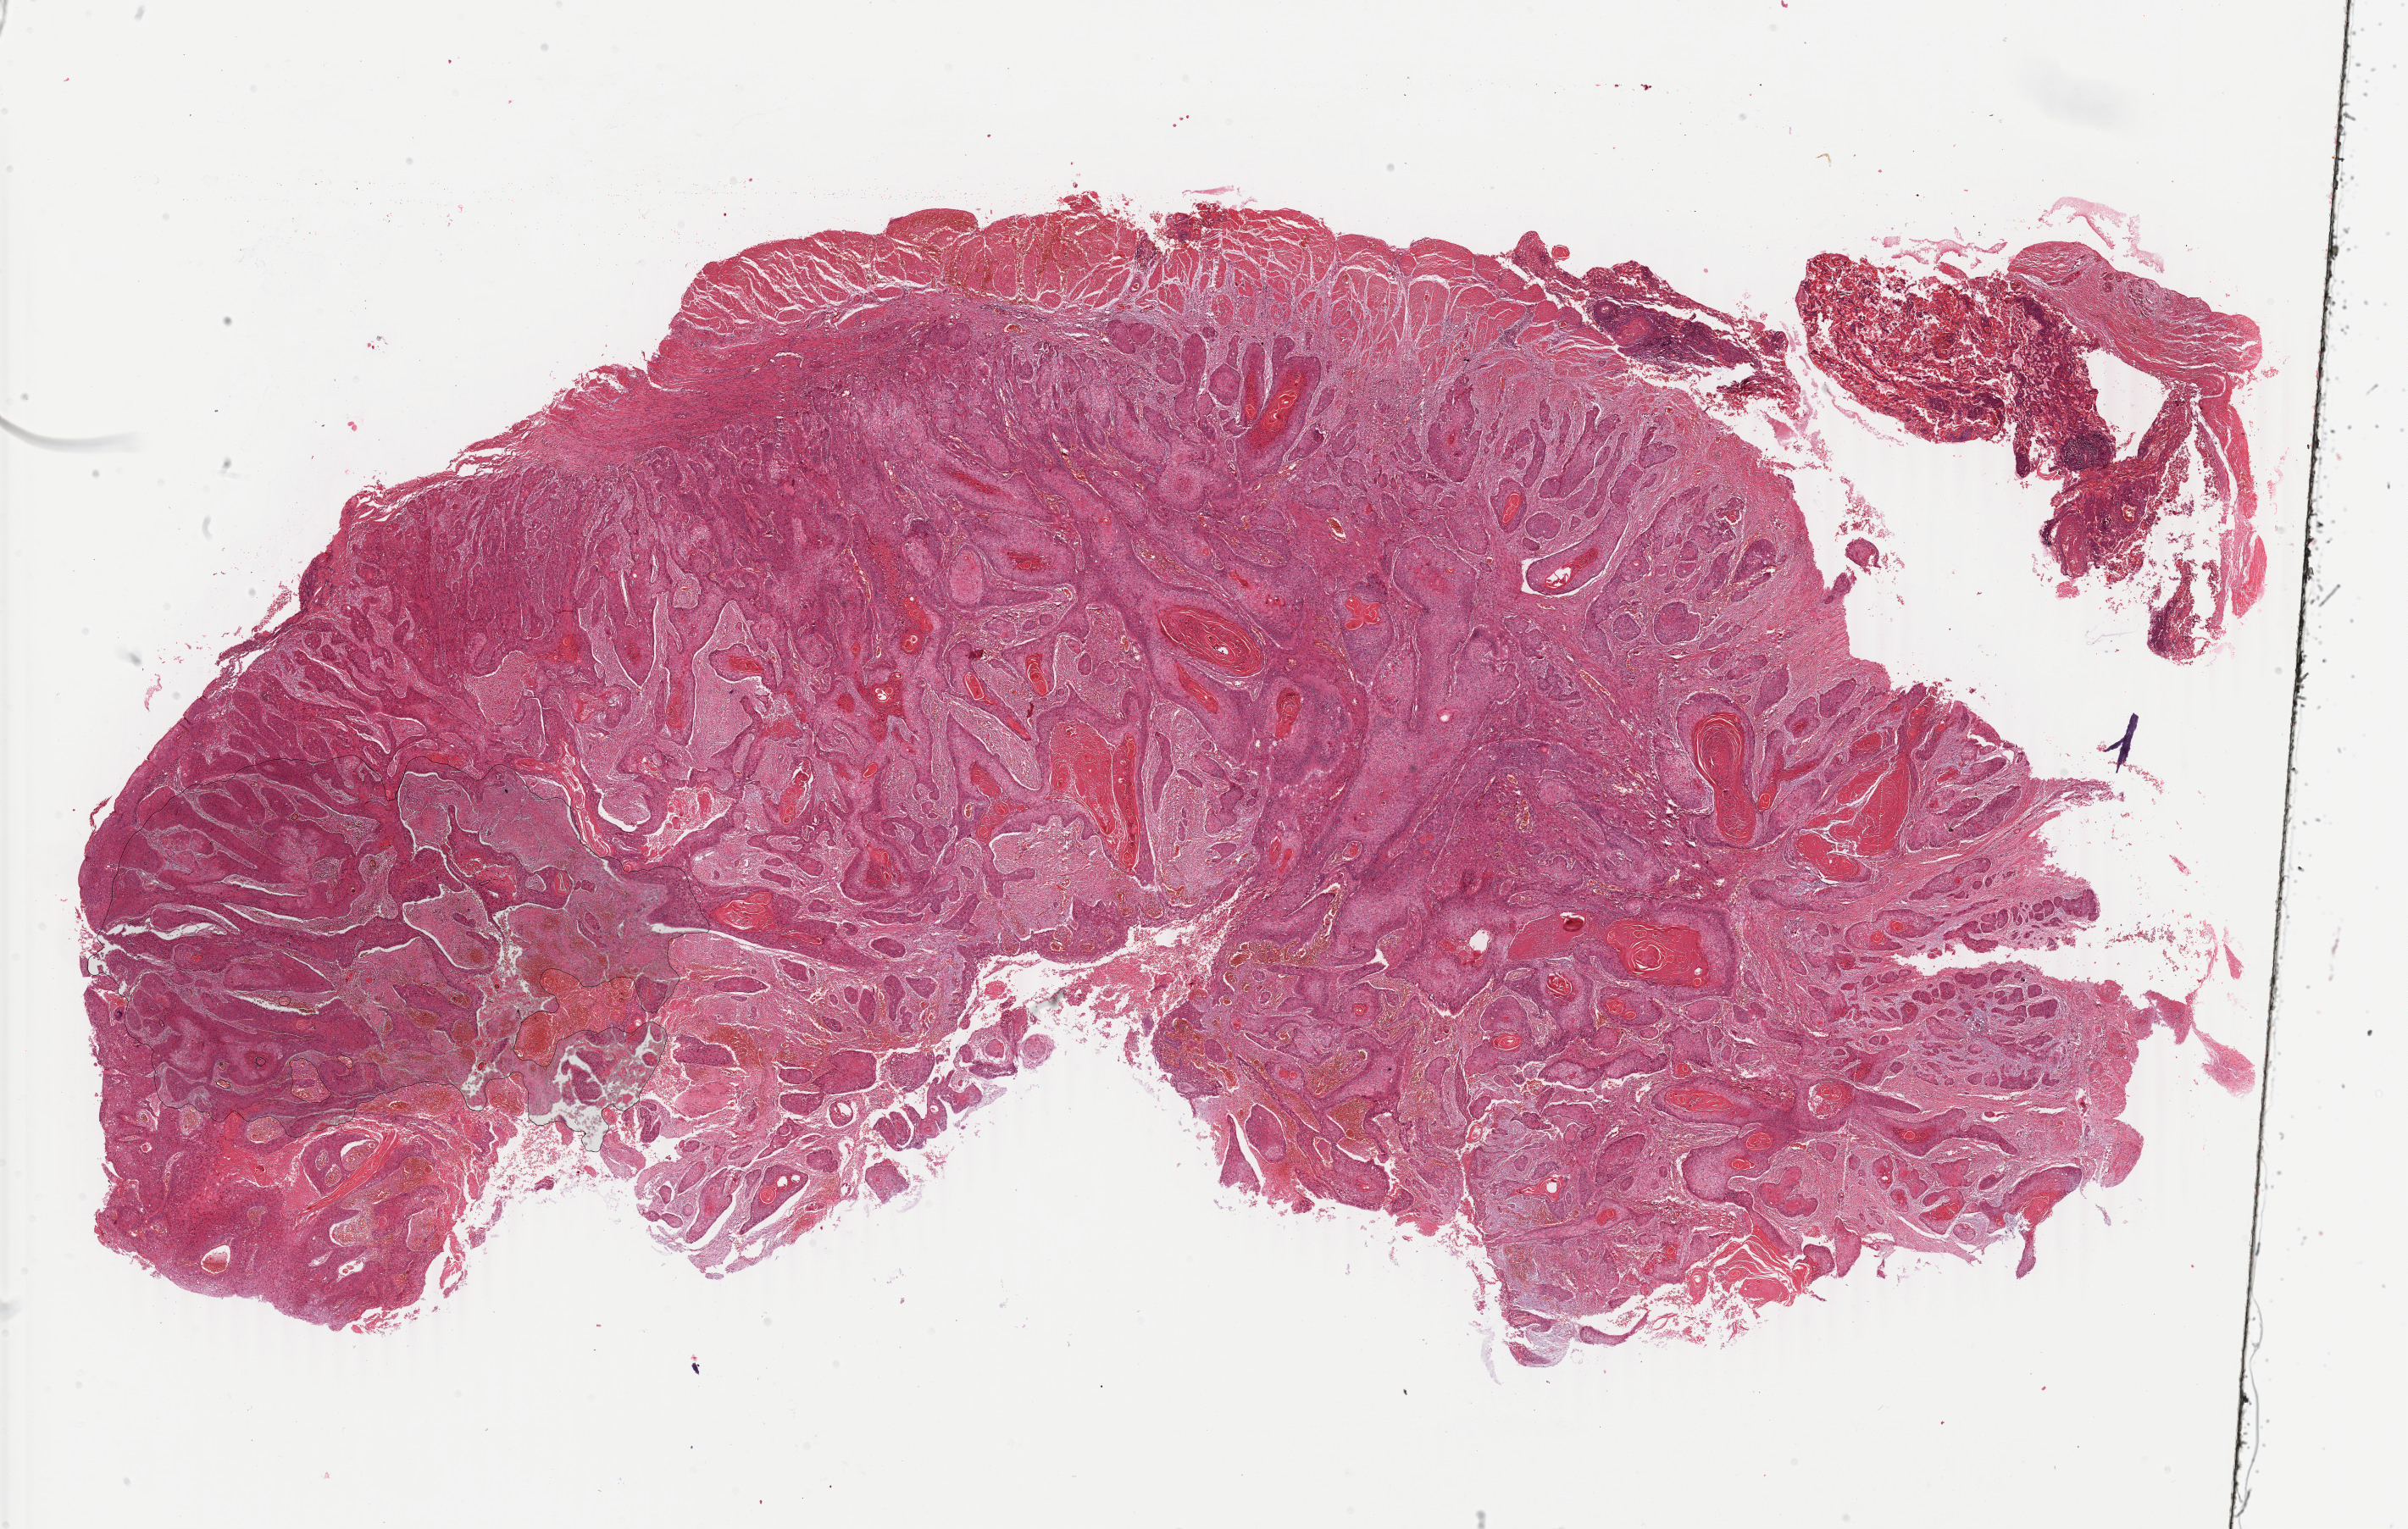
Hematoxylin and eosin (H&E) stained whole-slide image, a low-resolution overview of the entire scanned area, about 22.6 x 14.4 mm (from a 40x scan). Formalin-fixed paraffin-embedded (FFPE) diagnostic section. Sample: primary tumour, esophagus. Patient: male, age at initial diagnosis 62 years. Histologic grade: G1 (well differentiated).
• AJCC pathologic stage: IIA
• diagnosis: Squamous cell carcinoma, NOS (middle third of esophagus)